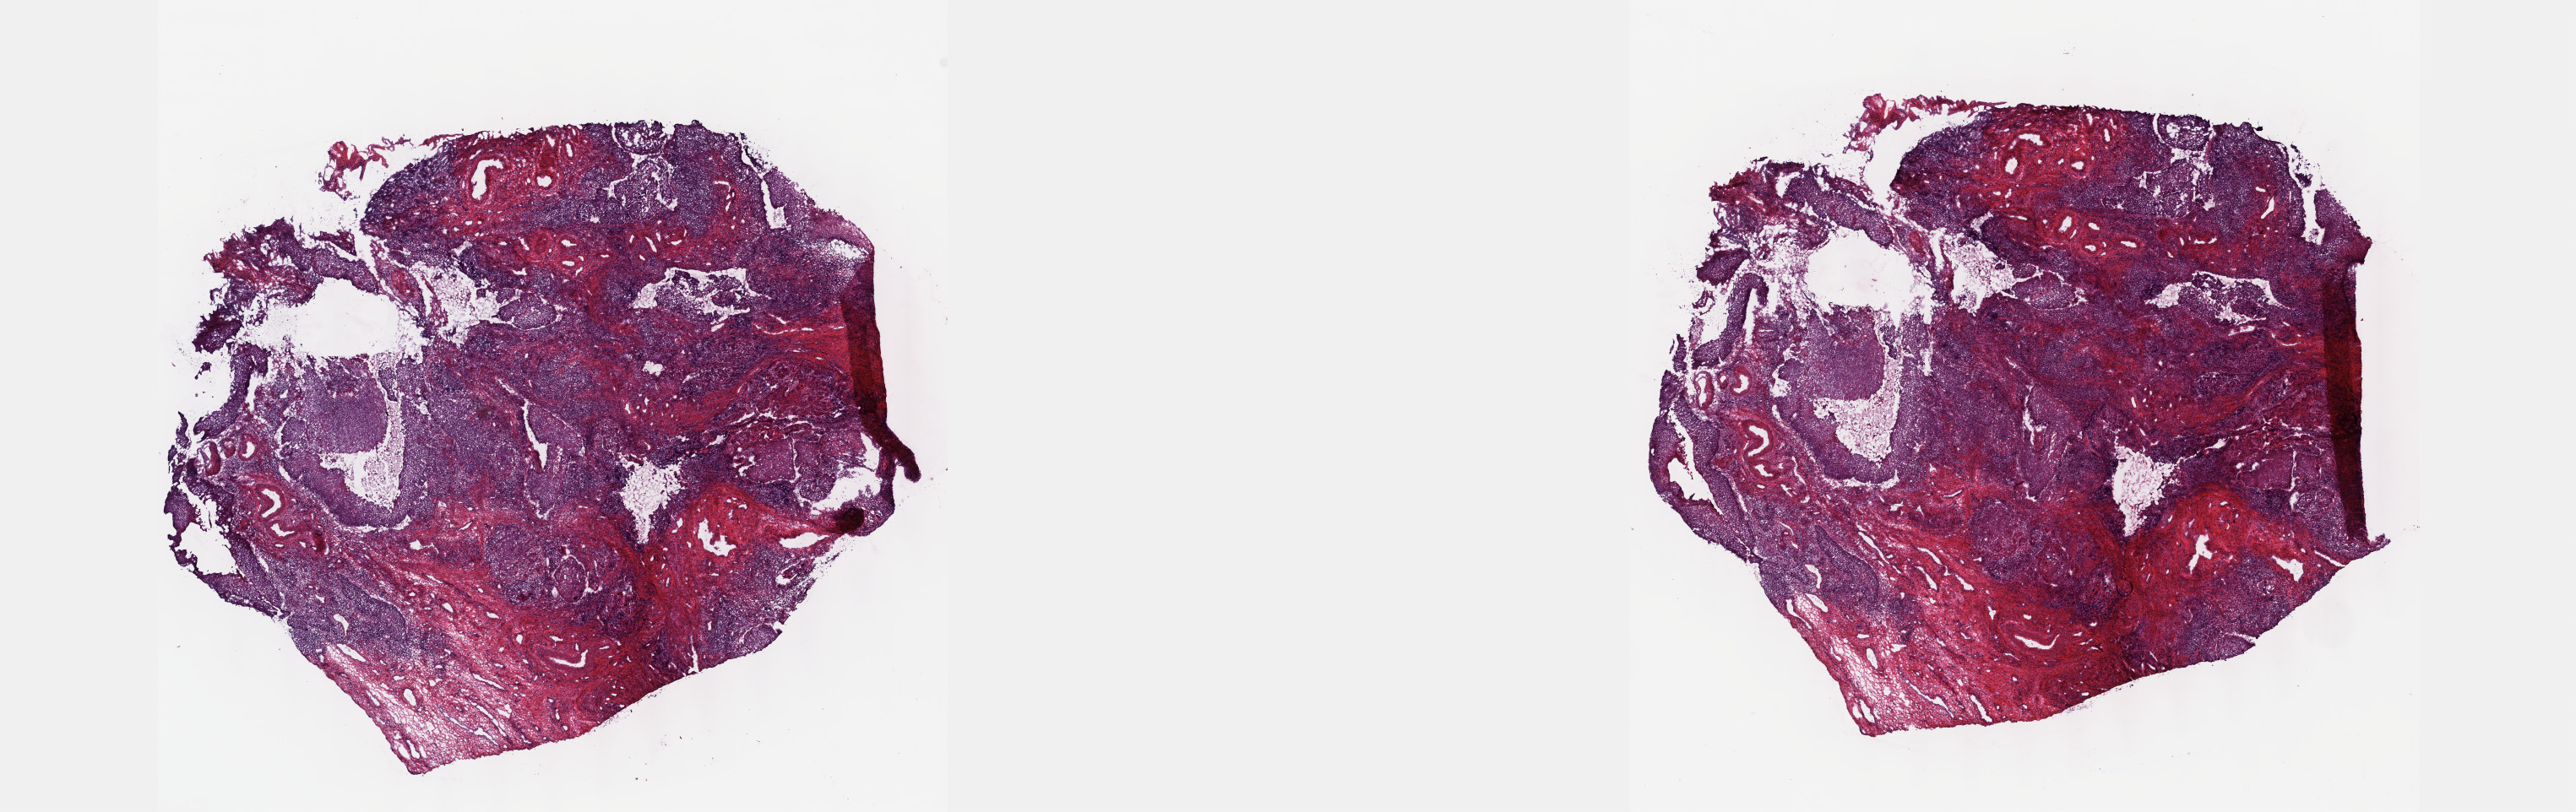
Digitized Hematoxylin and eosin (H&E) stained tissue section (whole slide), a low-resolution overview of the entire scanned area, about 24.6 x 7.8 mm (from a 40x scan); frozen section; cervix, primary tumour sample. Female, age 47 years at initial diagnosis.
Pathologic diagnosis: Squamous cell carcinoma, NOS (cervix uteri).